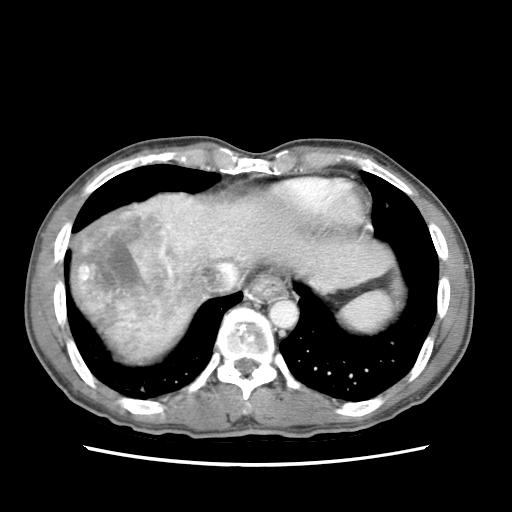
Contrast-enhanced abdominal CT (liver protocol), one axial slice; position 65 of 79 along the scan axis; reconstruction kernel STANDARD; 120 kVp; soft-tissue window (W 400 / L 40 HU); 2.5 mm slice thickness; 512 × 512 image matrix. From the clinical record (not read from this slice): diagnosis: hepatocellular carcinoma (patient treated with transarterial chemoembolisation; whether this scan precedes or follows treatment is not stated here); TNM stage (as recorded): Stage-IIIB; Child-Pugh class: A; tumour nodularity: multinodular.
Outlined on this slice (semi-automatically segmented with operator editing):
- abdominal aorta: bounding box <271,300,296,327> (left, top, right, bottom; pixels)
- liver parenchyma outside the tumour (the mass and vessels are separate outlines, so this box may not span the whole liver): <70,191,395,366>
- mass: <71,192,194,325>
- liver vessels: <129,241,221,327>